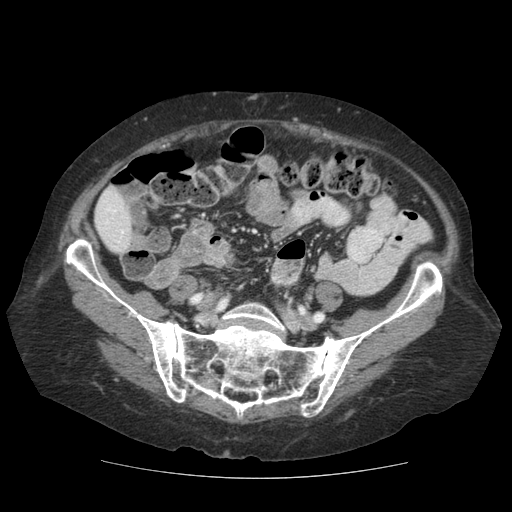
Contrast-enhanced abdominal CT (liver protocol), one axial slice. Slice 15 of 111 in the series (ordered by position). 140 kVp. Soft-tissue window (W 400 / L 40 HU). 512 × 512 image matrix, field of view 360 × 360 mm. From the clinical record (not read from this slice): diagnosis: hepatocellular carcinoma (patient treated with transarterial chemoembolisation; whether this scan precedes or follows treatment is not stated here); TNM stage (as recorded): Stage-I; Child-Pugh class: A; tumour differentiation: moderately-poorly differentiated; tumour nodularity: uninodular.
Annotated regions visible in this slice (semi-automatically segmented with operator editing):
- liver parenchyma outside the tumour (the mass and vessels are separate outlines, so this box may not span the whole liver): bounding box <94,186,132,252> (left, top, right, bottom; pixels)
- liver vessels: <108,208,124,233>